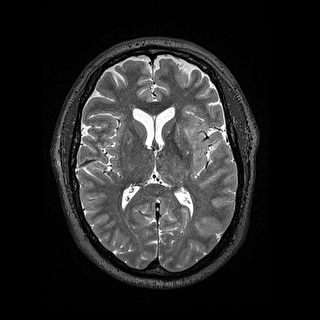
Brain MRI from a brain-tumour surgery series, one axial slice. Position 79 of 144 along the scan axis. 1.2 mm slice thickness. 320 × 320 image matrix. From the clinical record (not read from this slice): histopathology: Astrocytoma; WHO grade: 2; IDH mutation: yes.
Structures marked on this image (expert manual segmentation):
- tumour: bounding box <186,129,210,176> (left, top, right, bottom; pixels)